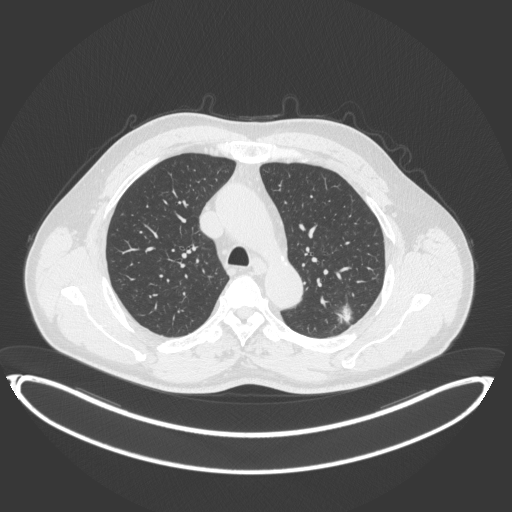
Chest CT, one axial slice; position 257 of 399 along the scan axis; reconstruction kernel B31f; 120 kVp; lung window (W 1500 / L -600 HU); 1 mm slice thickness; 512 × 512 image matrix, field of view 469 × 469 mm. Male patient, age 58 years. Case-level facts recorded for this patient, not image findings: clinical TNM (as recorded): T1c N0 M0.
Structures marked on this image (bounding box drawn by a radiologist):
- lung tumour (recorded histology: adenocarcinoma): bounding box (x1, y1, x2, y2) in pixels: (330, 300, 357, 328)